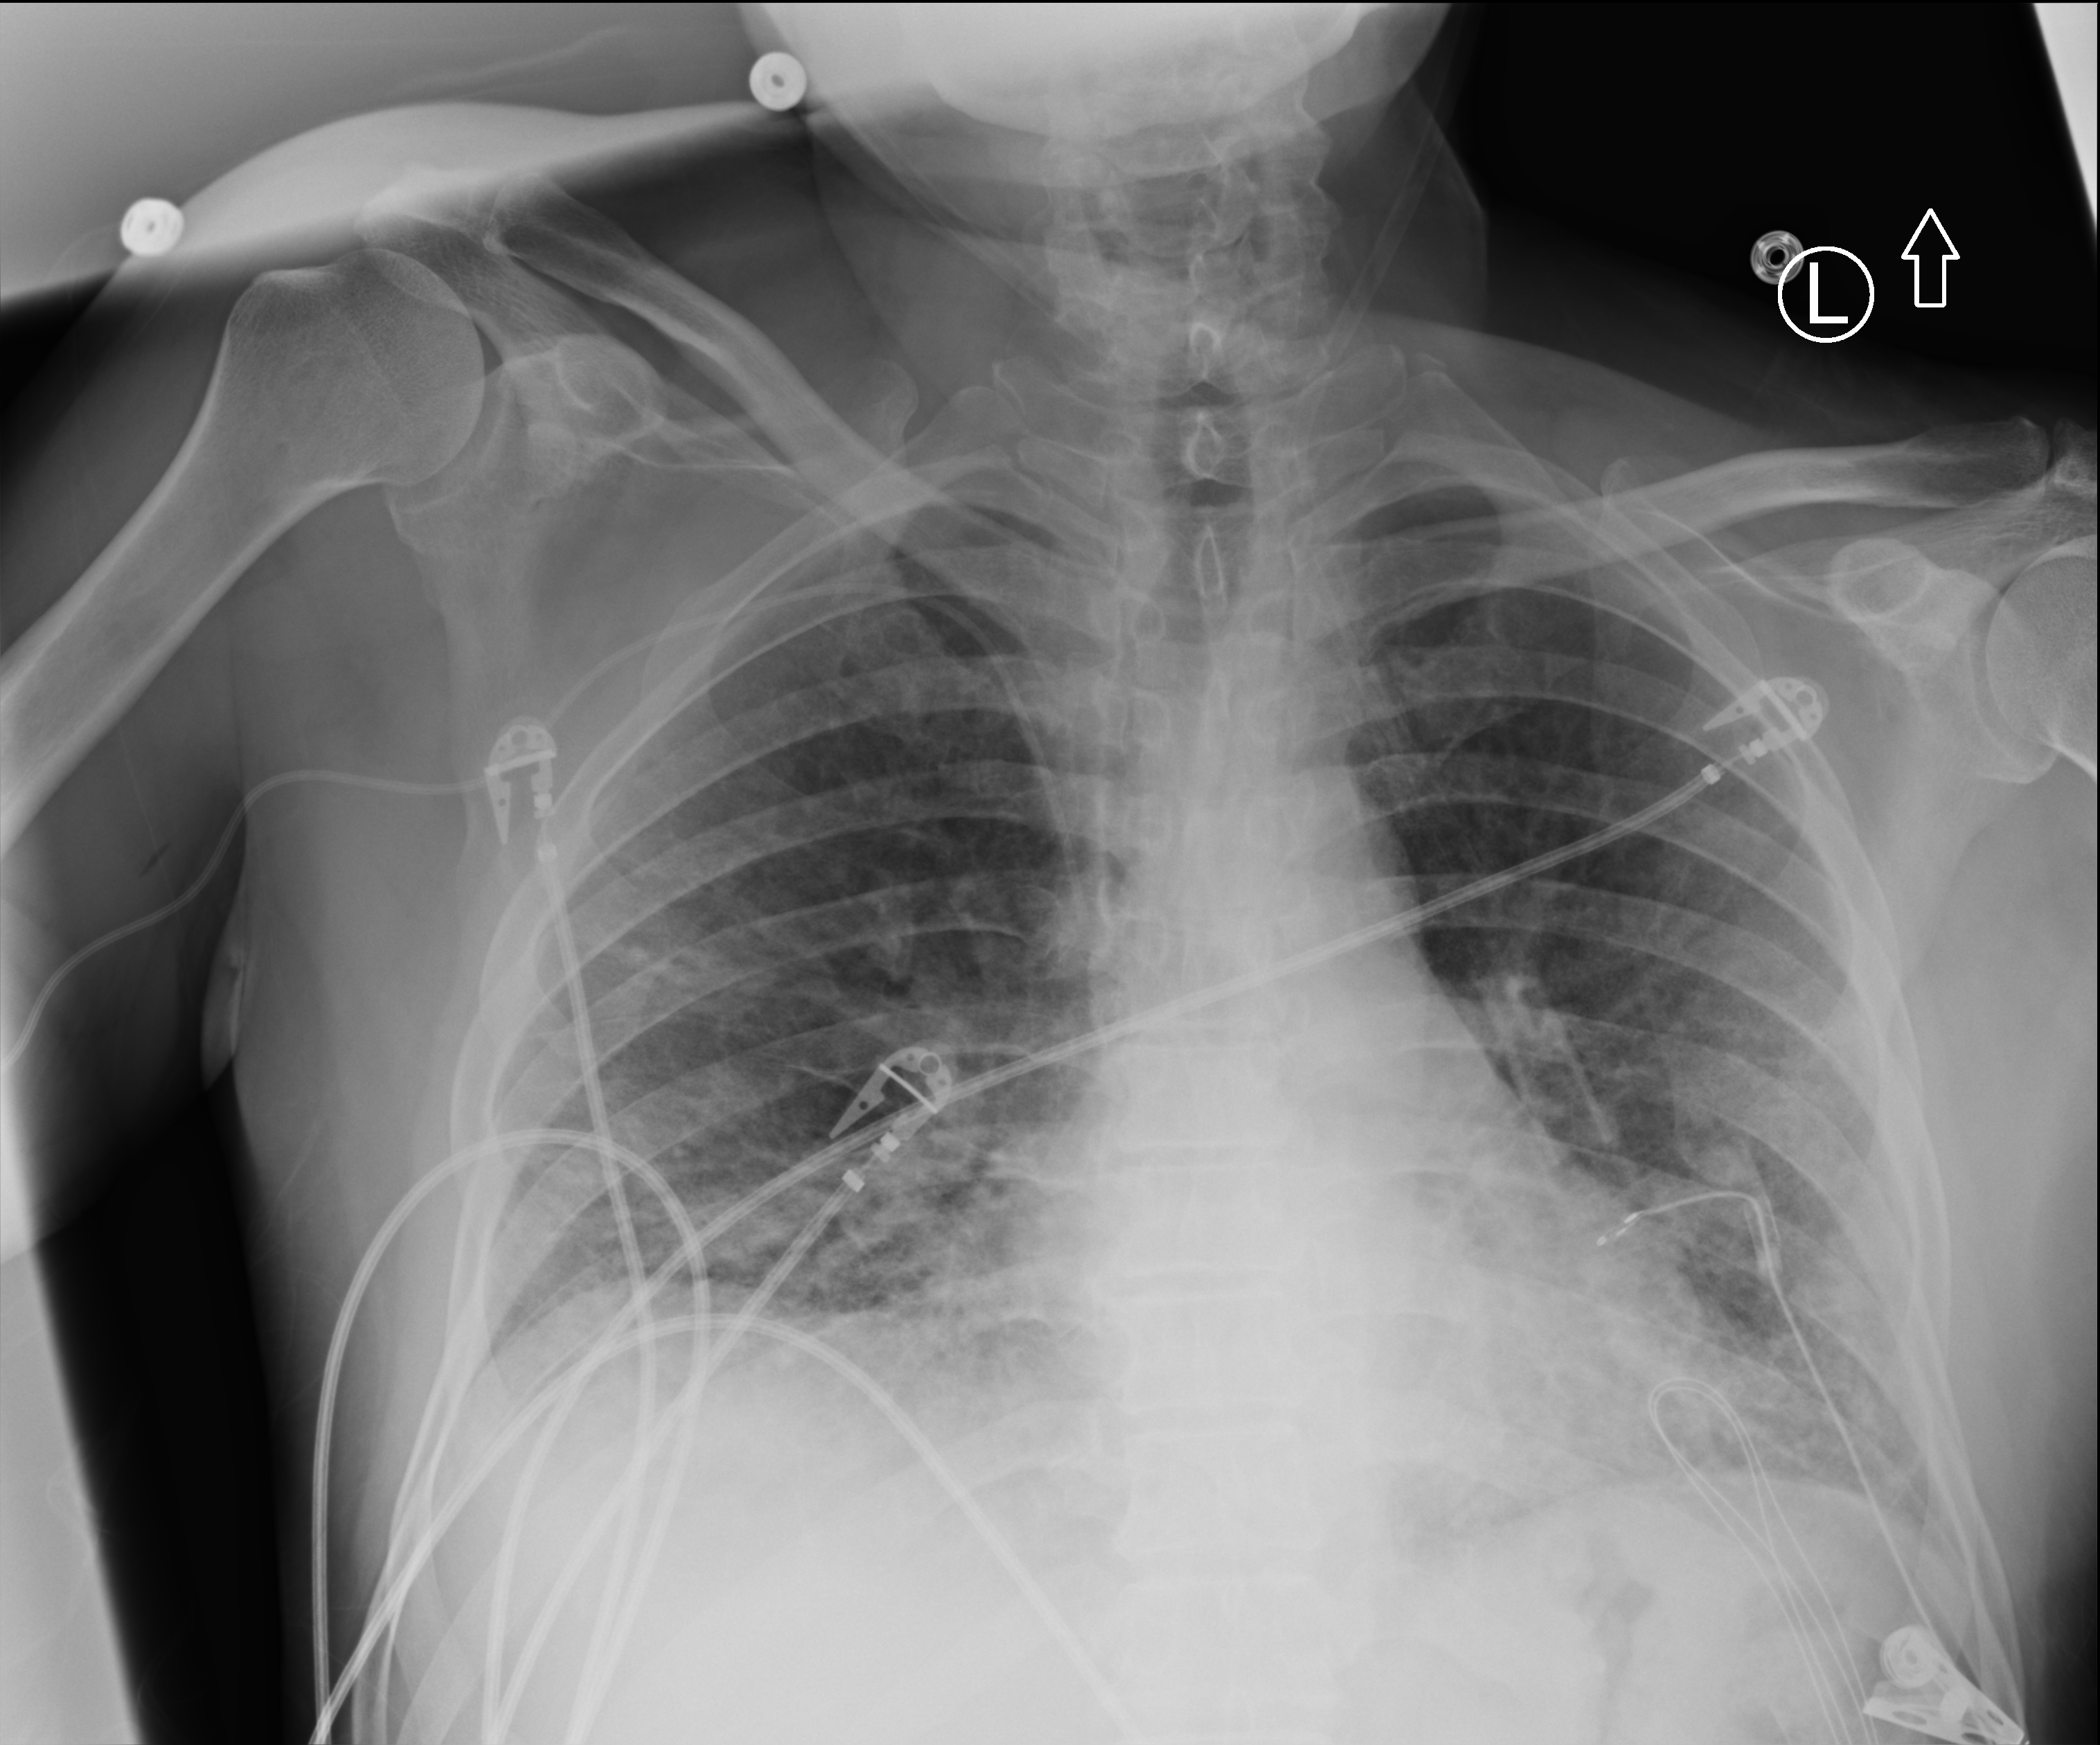
Bedside chest radiograph (computed radiography); anteroposterior (AP) projection. Male patient hospitalised with COVID-19, age 18–59 years.
Hospital-stay facts (about this admission, not read from this image; timing relative to this image not recorded):
- admitted to intensive care during this hospital stay: yes
- length of hospital stay: 38 days
- mechanically ventilated during this hospital stay: no